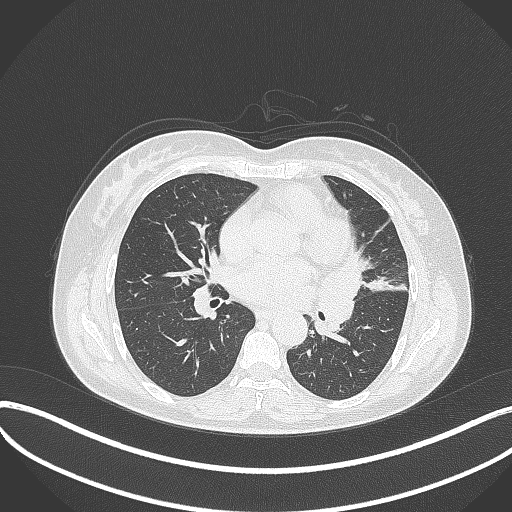
Chest CT, one axial slice. Position 174 of 373 along the scan axis. 120 kVp. Lung window (W 1500 / L -600 HU). 1 mm slice thickness. 512 × 512 image matrix. Patient: female, 54 years. Case-level facts recorded for this patient, not image findings: clinical TNM (as recorded): T2a N1 M0; histopathological grade: G3.
Outlined on this slice (rectangle marked by the reading radiologist):
- lung tumour (recorded histology: small cell carcinoma): bounding box <315,260,370,338> (left, top, right, bottom; pixels)